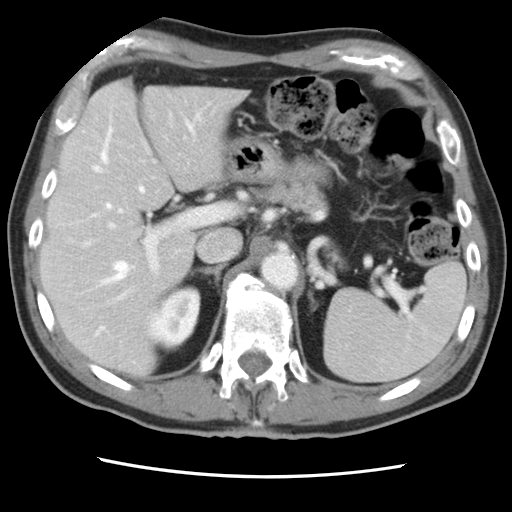
Contrast-enhanced abdominal CT, one axial slice. Position 54 of 83 along the scan axis. Intravenous contrast given. Soft-tissue window (W 400 / L 40 HU). 5 mm slice thickness. 512 × 512 image matrix, field of view 321 × 321 mm. Male patient, age 69 years. From the clinical record (not read from this slice): diagnosis: colorectal cancer liver metastases, imaged before liver resection; multiple liver metastases: yes; largest metastasis: 3.5 cm.
Annotated regions visible in this slice (manually delineated by an expert):
- hepatic veins: box from (x=94, y=122) to (x=193, y=333) px
- liver: (x=42, y=81)–(x=243, y=376)
- planned liver remnant (the part of the liver to remain after resection): (x=42, y=138)–(x=195, y=376)
- portal vein (with intrahepatic branches): (x=82, y=135)–(x=230, y=301)